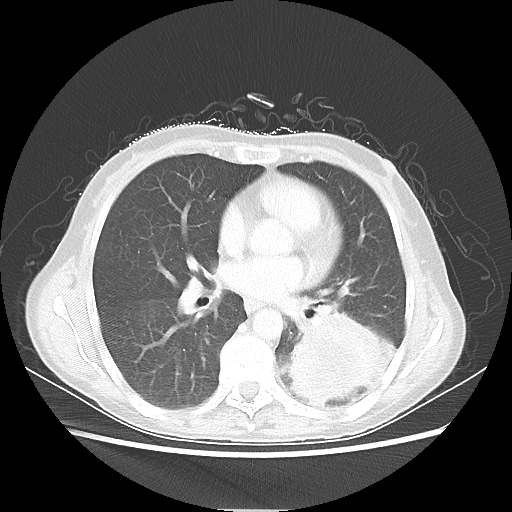
Chest CT, one axial slice. Slice 28 of 56 in the series (ordered by position). Reconstruction kernel LUNG. Lung window (W 1500 / L -600 HU). 5 mm slice thickness. 512 × 512 image matrix, field of view 360 × 360 mm. Patient: female, 53 years. Case-level facts recorded for this patient, not image findings: clinical TNM (as recorded): T3 N0 M0.
Structures marked on this image (bounding box drawn by a radiologist):
- lung tumour (recorded histology: adenocarcinoma): bounding box (x1, y1, x2, y2) in pixels: (293, 313, 398, 407)